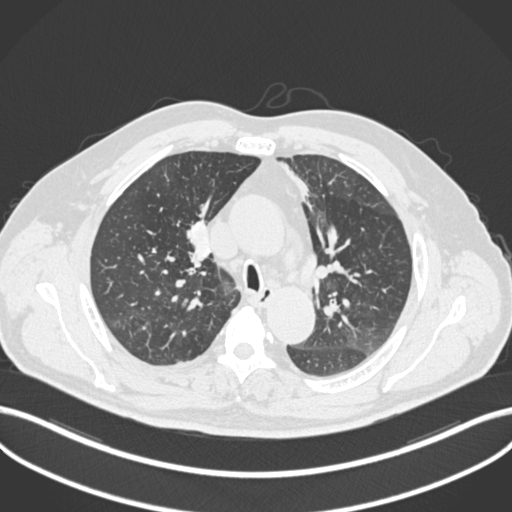
Chest CT, one axial slice; slice 134 of 255 in the series (ordered by position); 120 kVp; lung window (W 1500 / L -600 HU); 512 × 512 image matrix, field of view 400 × 400 mm. Male patient, age 60 years. Case-level facts recorded for this patient, not image findings: clinical TNM (as recorded): T1b N1 M0.
Structures marked on this image (bounding box drawn by a radiologist):
- lung tumour (recorded histology: squamous cell carcinoma): box from (x=183, y=215) to (x=216, y=268) px